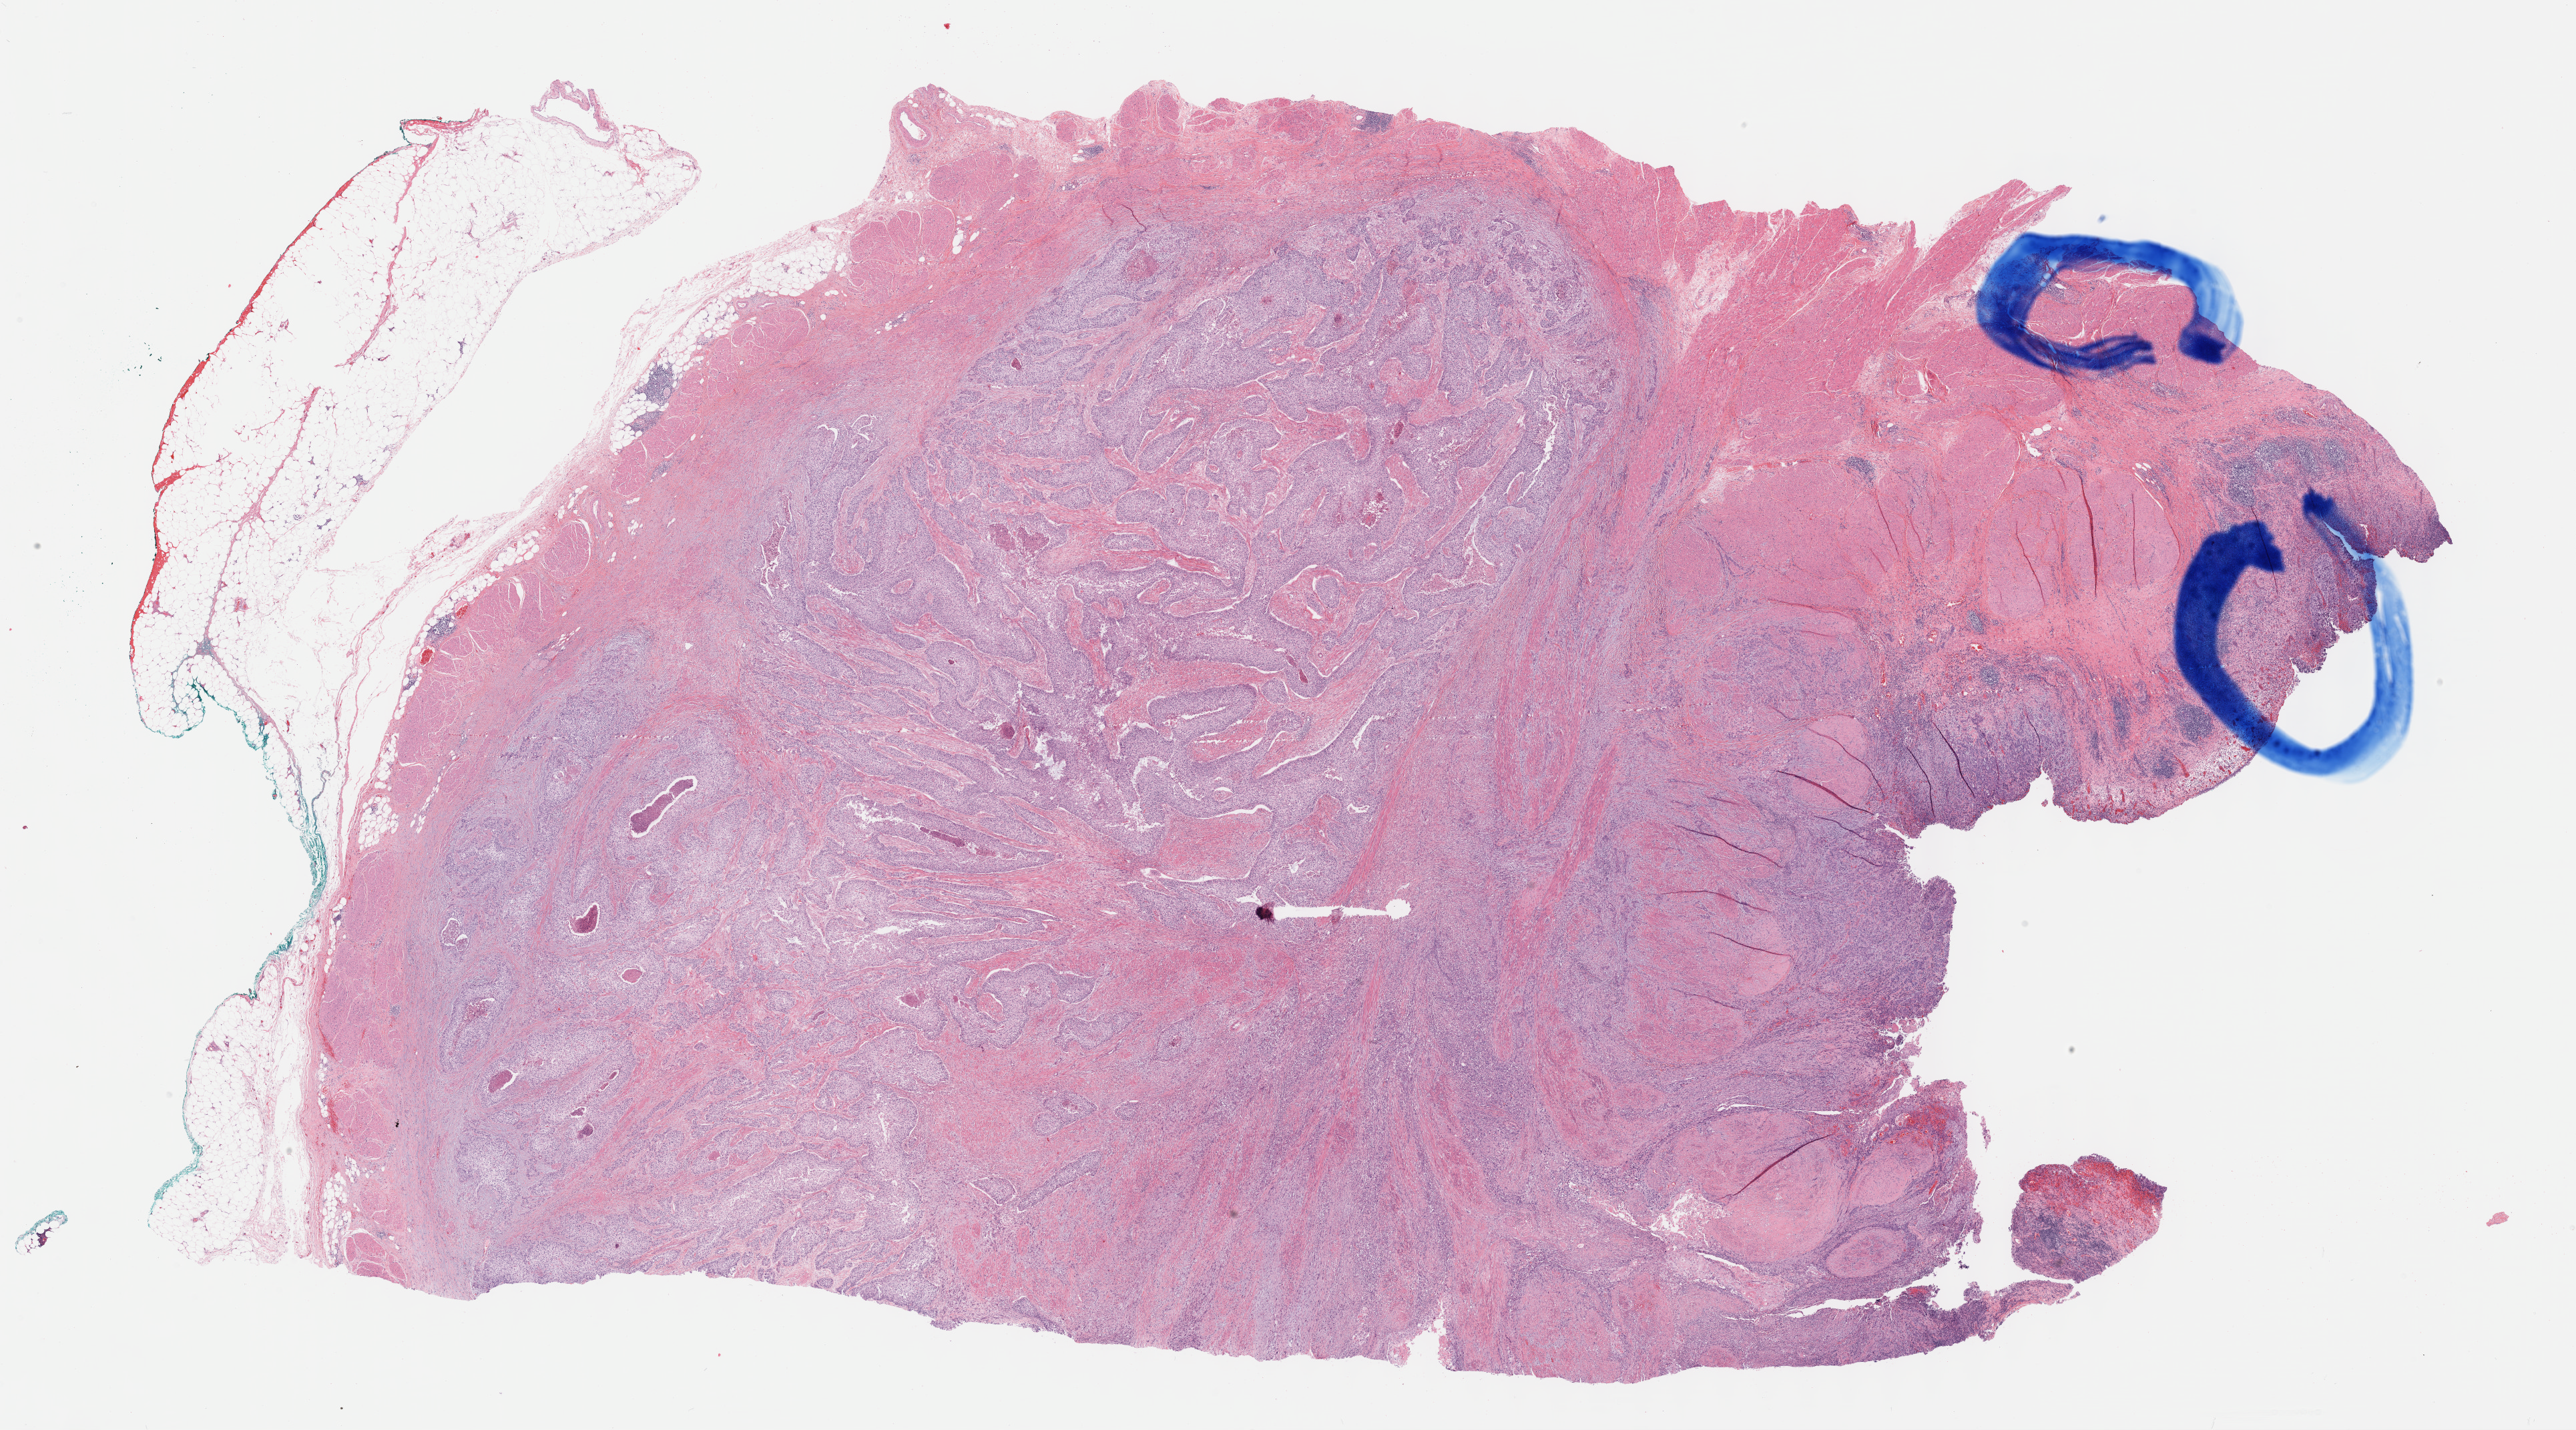
Hematoxylin and eosin (H&E) stained whole-slide image, whole scanned area (about 31.2 x 17.3 mm) shown as a low-resolution overview, formalin-fixed paraffin-embedded (FFPE) diagnostic section, sample: primary tumour, bladder. Patient: male, age at initial diagnosis 86 years. Histologic grade: high grade.
TNM: T2b N2 MX. AJCC pathologic stage: IV (7th edition). Pathologic diagnosis: Transitional cell carcinoma.